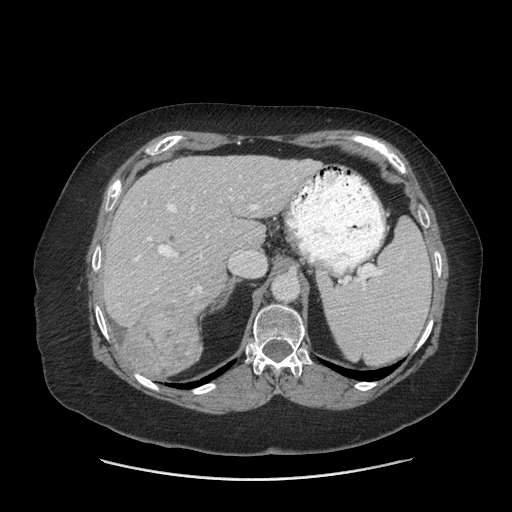
Contrast-enhanced abdominal CT (liver protocol), one axial slice; position 46 of 69 along the scan axis; 140 kVp; soft-tissue window (W 400 / L 40 HU); 2.5 mm slice thickness; 512 × 512 image matrix. Case-level facts recorded for this patient, not image findings: diagnosis: hepatocellular carcinoma (patient treated with transarterial chemoembolisation; whether this scan precedes or follows treatment is not stated here); TNM stage (as recorded): Stage-IIIB; Child-Pugh class: A; tumour differentiation: moderately differentiated; tumour nodularity: multinodular.
Structures marked on this image (semi-automatically segmented with operator editing):
- liver parenchyma outside the tumour (the mass and vessels are separate outlines, so this box may not span the whole liver): box from (x=102, y=156) to (x=321, y=352) px
- mass: (x=124, y=302)–(x=201, y=377)
- liver vessels: (x=134, y=176)–(x=297, y=295)